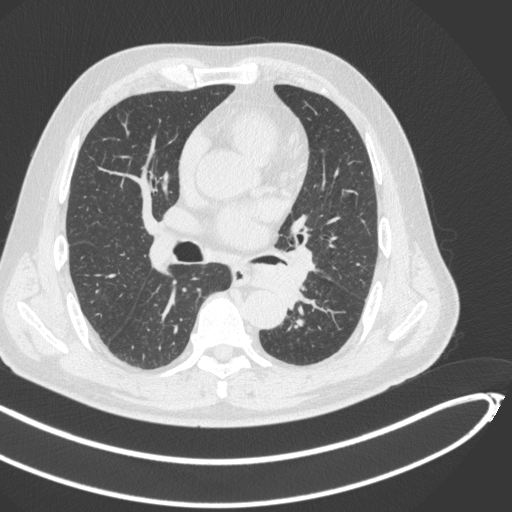
Chest CT, one axial slice; reconstruction kernel B31f; 120 kVp; lung window (W 1500 / L -600 HU); 1 mm slice thickness; 512 × 512 image matrix, field of view 400 × 400 mm. Male patient, age 64 years. Case-level facts recorded for this patient, not image findings: clinical TNM (as recorded): T1c N0 M0; histopathological grade: G2.
Structures marked on this image (bounding box drawn by a radiologist):
- lung tumour (recorded histology: squamous cell carcinoma): bounding box (x1, y1, x2, y2) in pixels: (253, 261, 307, 300)